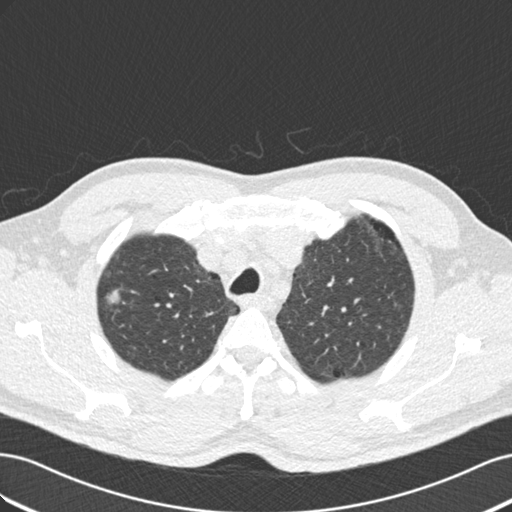
Chest CT (low-dose screening protocol), one axial image, second screening round (one year after baseline), lung window (W 1500 / L -600 HU), 2 mm slice thickness, 120 kVp. Male, age 56 years at enrolment. Current smoker at enrolment.
Lesion marked by an expert reader, bounding box [x1, y1, x2, y2] px = [83, 281, 130, 318]. Screening reader's record for this exam (one nodule recorded; not confirmed to be the boxed lesion): non-calcified nodule or mass ≥4 mm, right upper lobe, 13 × 12 mm, smooth margins, mixed attenuation, pre-existing on the prior screen: yes; interval growth: yes. Official screen result: positive, change unspecified: nodule(s) >= 4 mm or enlarging nodule(s), mass(es), or other non-specific abnormalities suspicious for lung cancer.